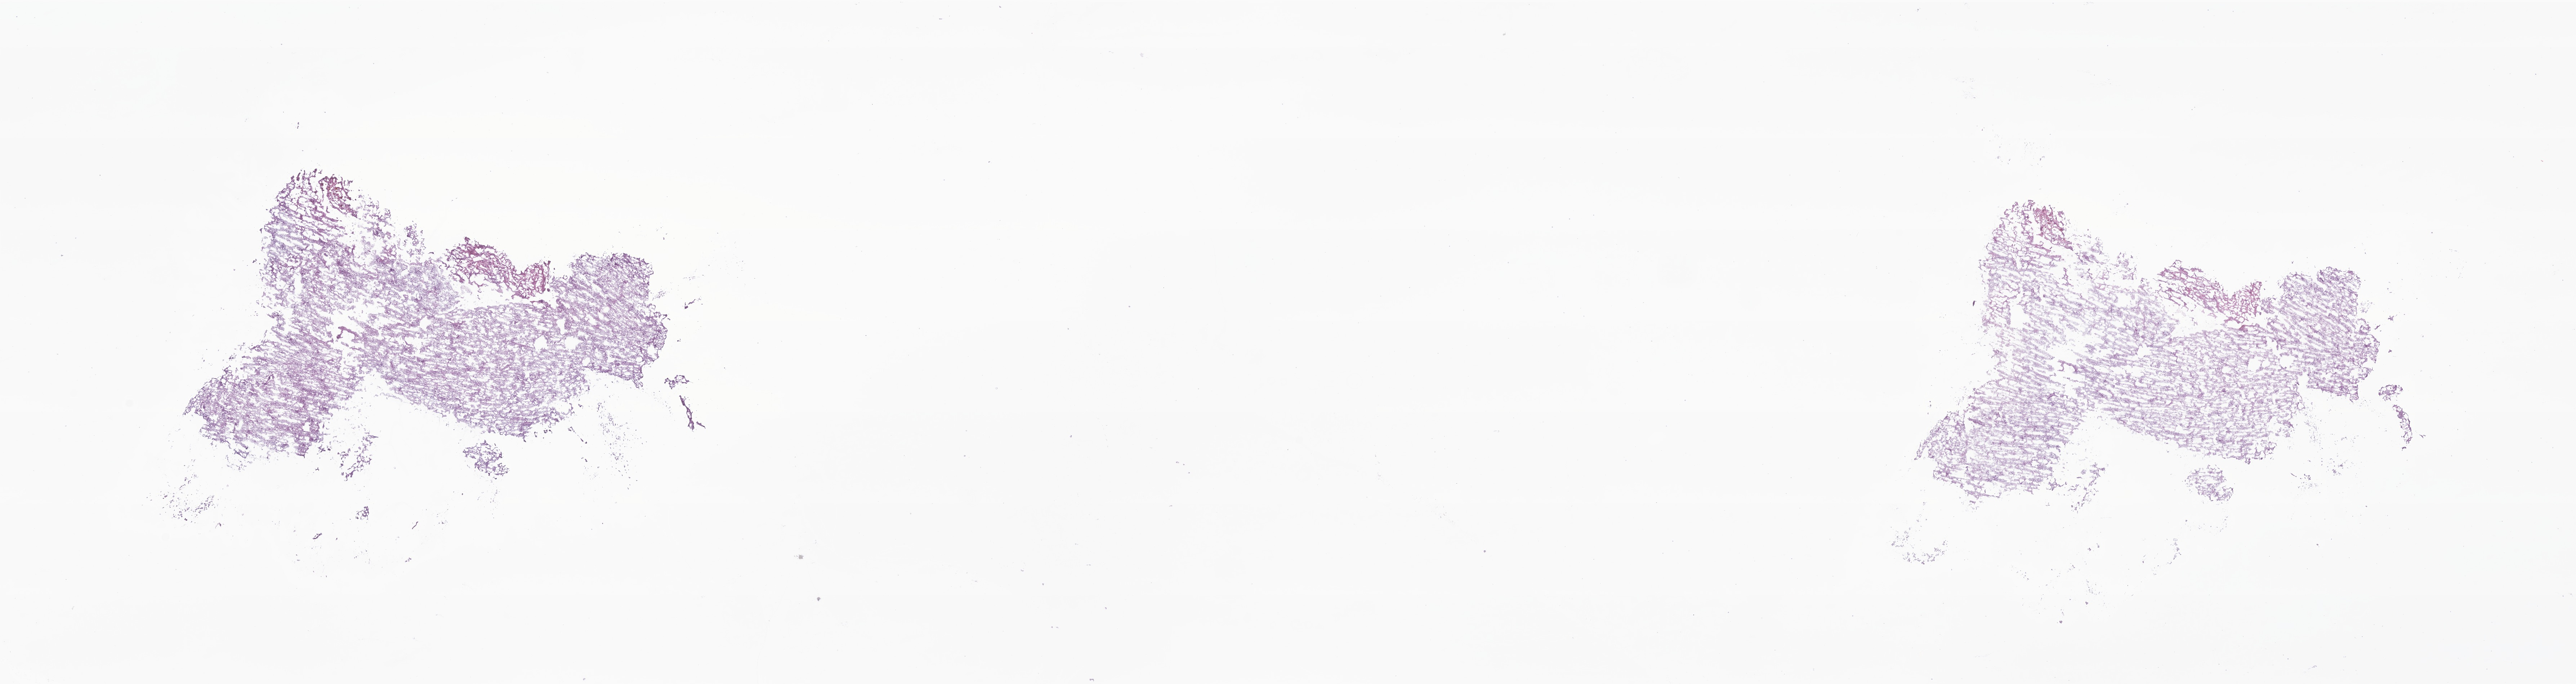
Digitized hematoxylin and eosin (H&E)-stained section of tumor tissue from the brain — low-resolution overview of the scanned area, about 30.1 x 8.0 mm, frozen section (OCT-embedded). Patient female; age 42 months.
Diagnosis: Pilocytic astrocytoma.